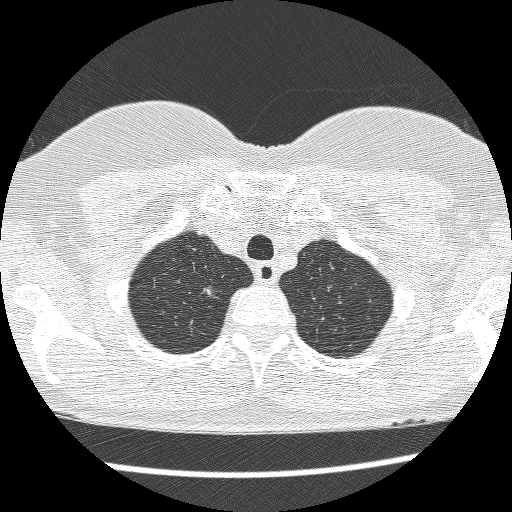
Chest CT (low-dose screening protocol), one axial image, baseline annual screen, lung window (W 1500 / L -600 HU). Female participant, aged 61 years at enrolment.
- Expert reader's lesion annotation, bounding box <191,279,229,306> (left, top, right, bottom; pixels).
- The exam's reader record, not a measurement of the box and not confirmed to be the same lesion: non-calcified nodule or mass ≥4 mm, right upper lobe, 7 × 6 mm, poorly defined margins, mixed attenuation.